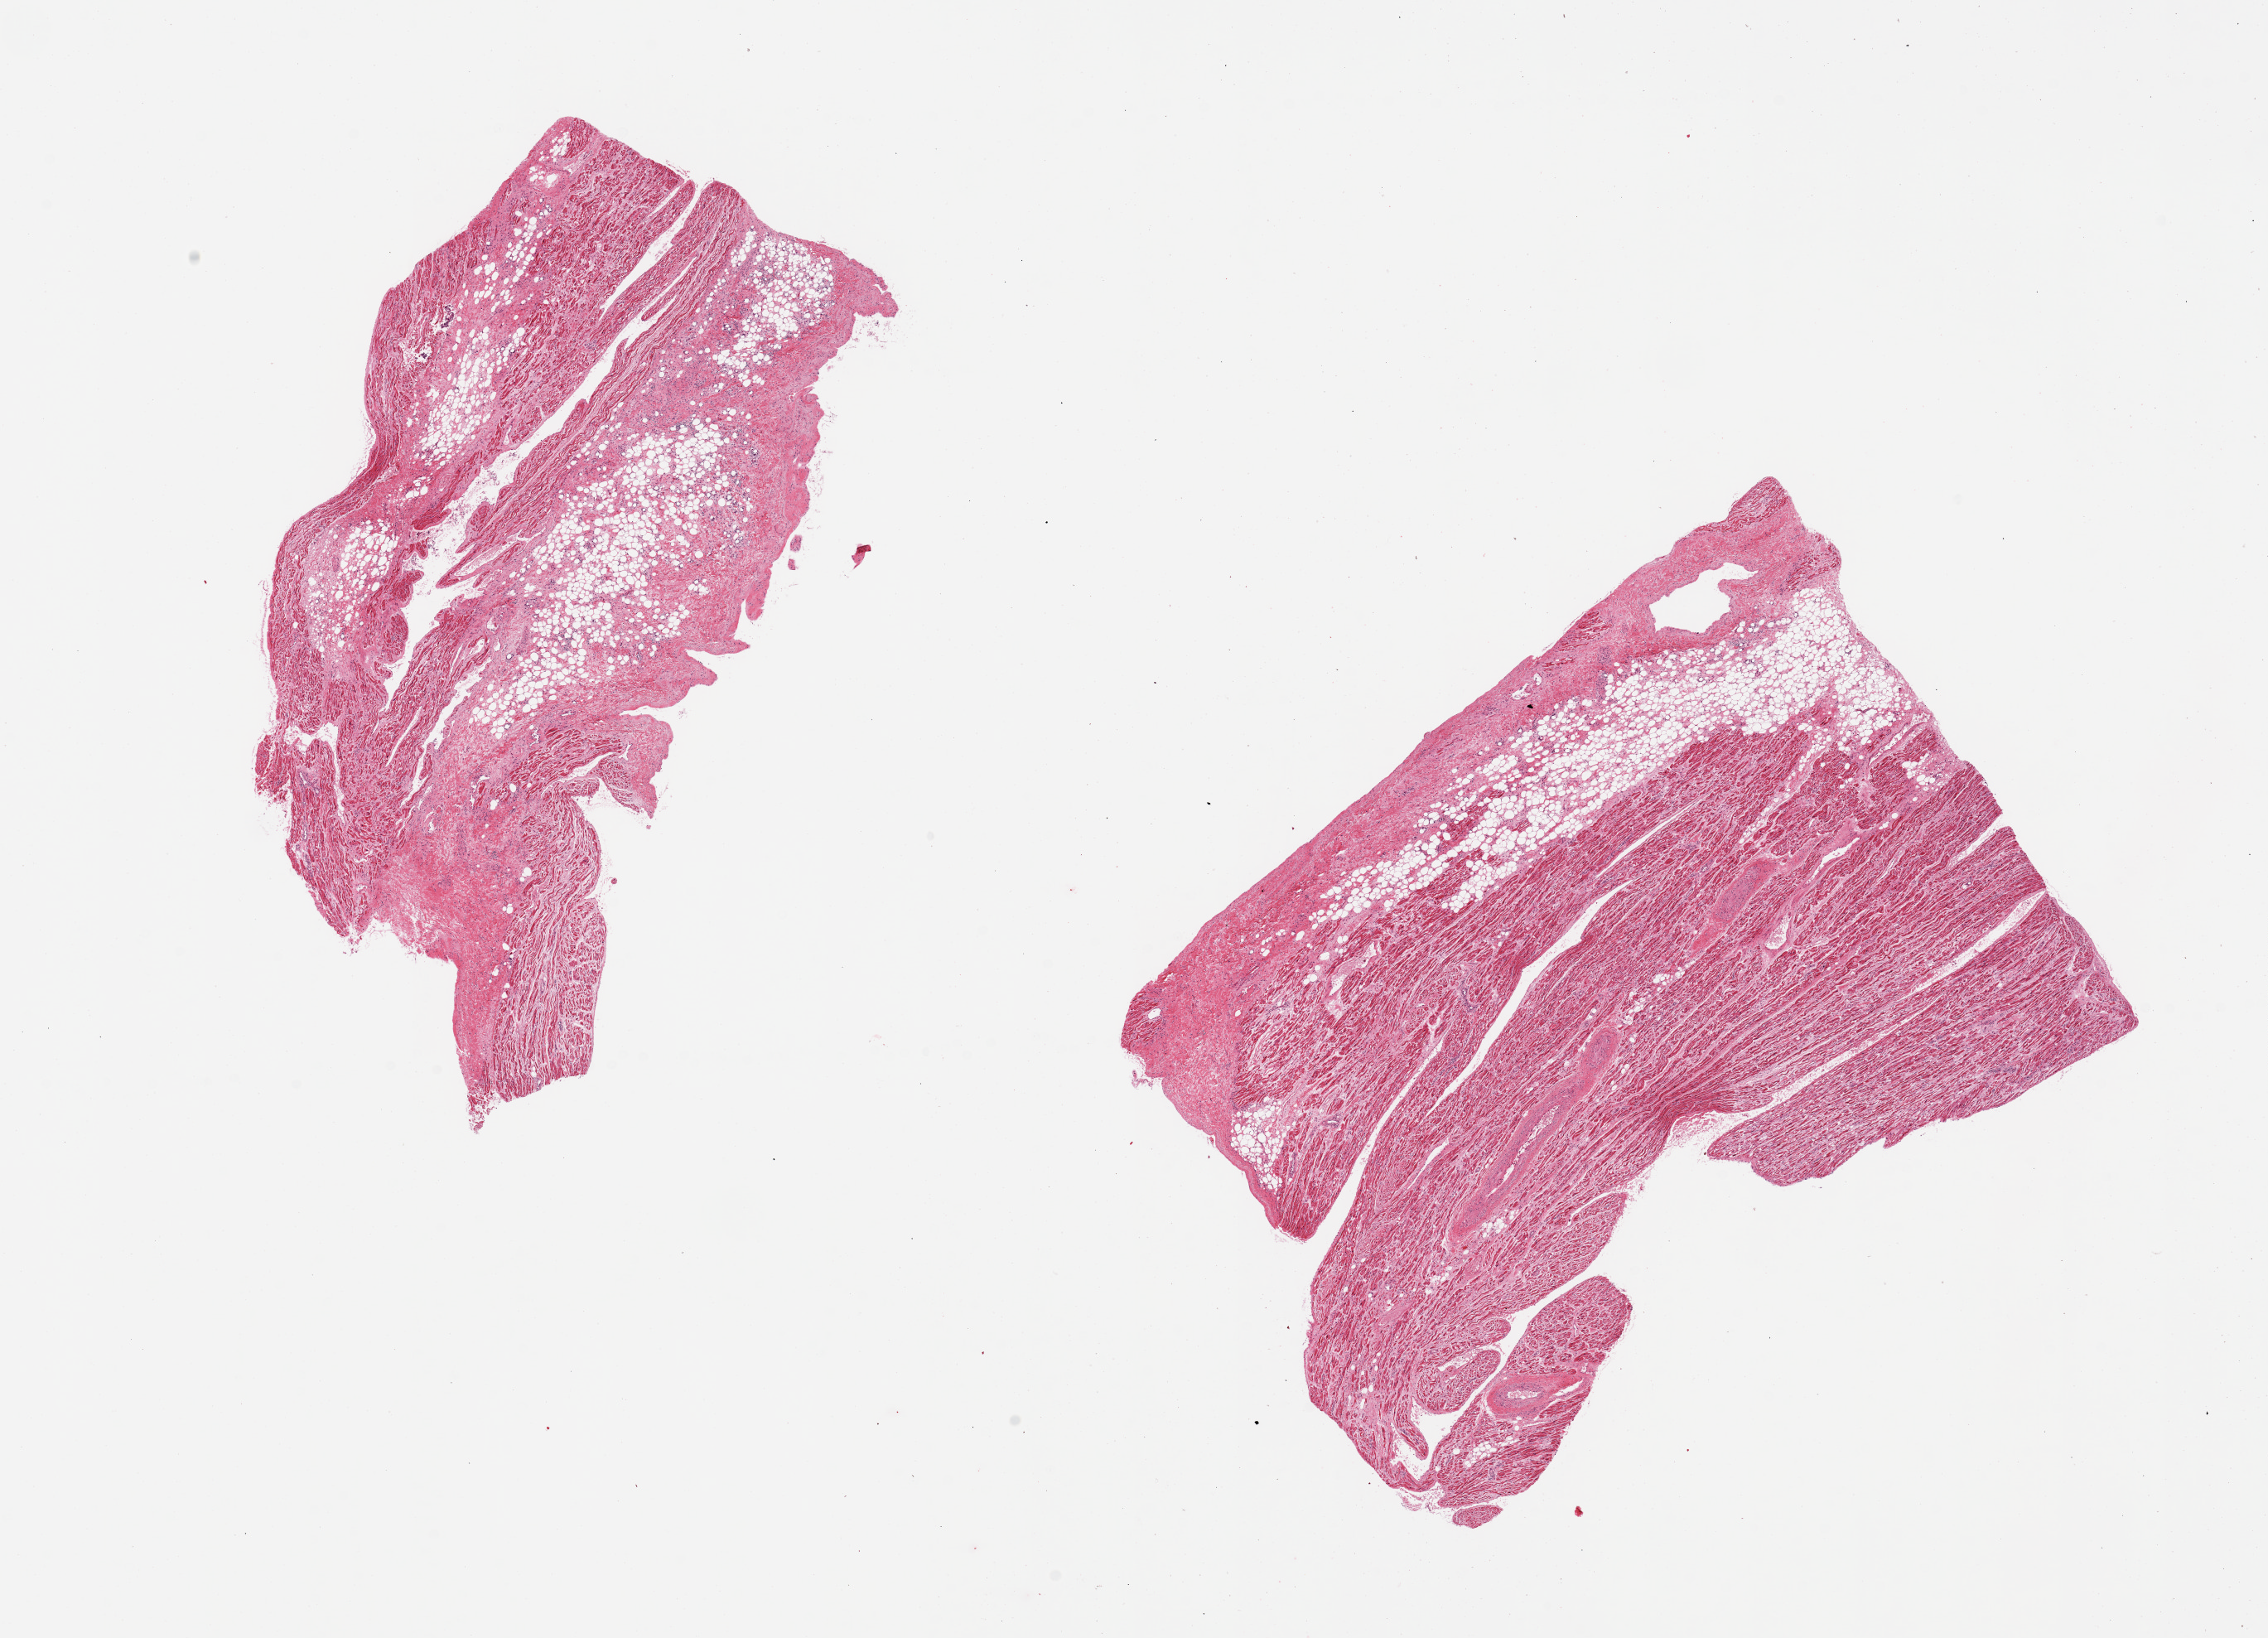
Whole-slide image, hematoxylin and eosin (H&E) stain — low-resolution overview of the scanned area, about 21.7 x 15.6 mm (from a 20x scan), PAXgene-fixed, paraffin-embedded tissue, target tissue: auricular appendage, tissue donor sample. Male donor.
* review note (as recorded): 2 pieces